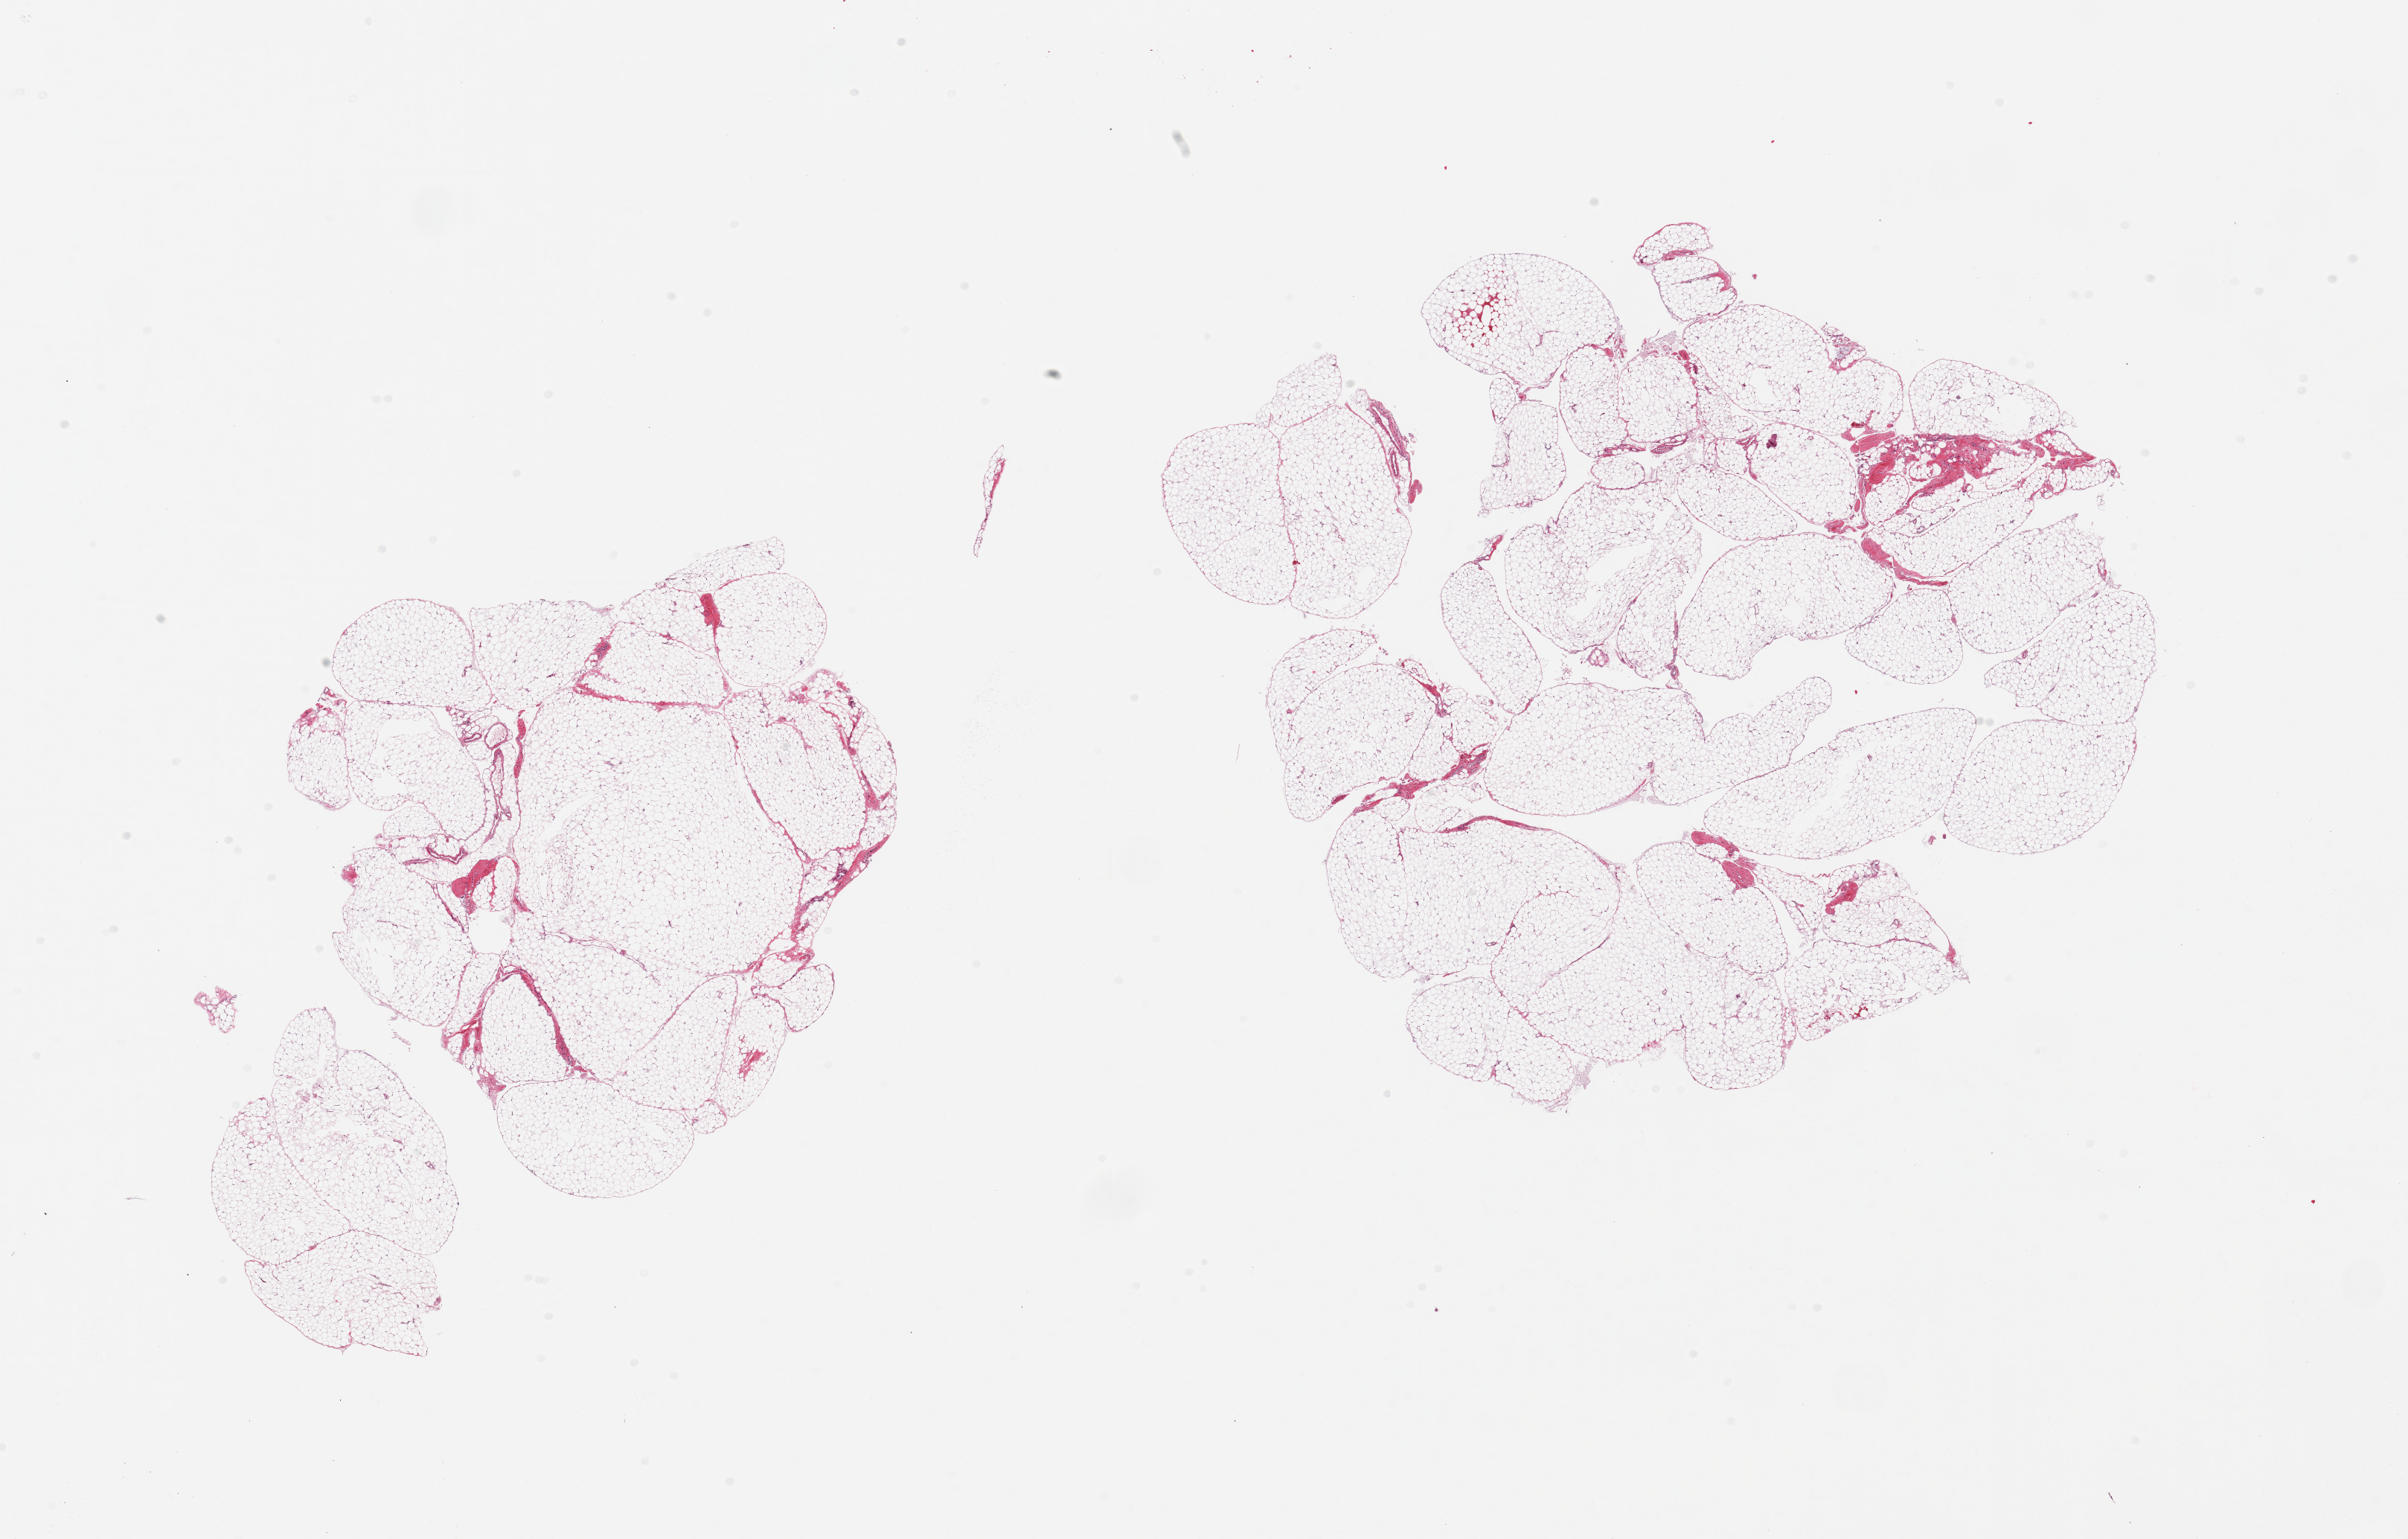
Haematoxylin and eosin whole-slide image — low-resolution overview of the scanned area, about 25.6 x 16.4 mm; PAXgene-fixed paraffin-embedded (PFPE) section; sampled site (target tissue): omentum; tissue donor sample.
Review note (as recorded): 2 pieces; <5% fibrous content.